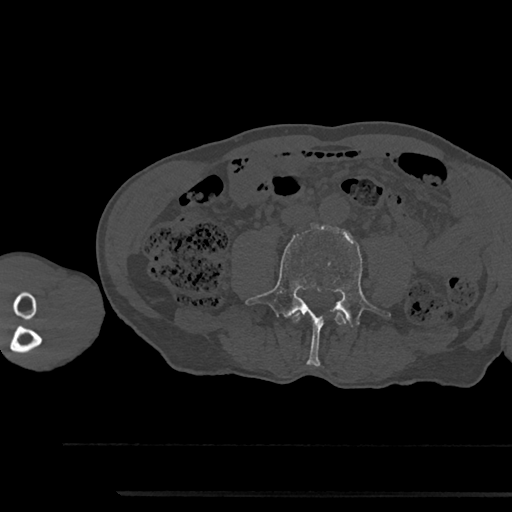
CT including the spine, one axial slice. Position 426 of 797 along the scan axis. Bone window (W 1800 / L 400 HU). 512 × 512 image matrix, field of view 367 × 367 mm. Patient: male, 79 years. Case-level facts recorded for this patient, not image findings: primary cancer: prostate.
Annotated regions visible in this slice (semi-automatic segmentation, software-assisted and operator-edited):
- L3 vertebra: bounding box [x1, y1, x2, y2] px = [293, 312, 346, 325]
- L4 vertebra: [245, 225, 391, 366]